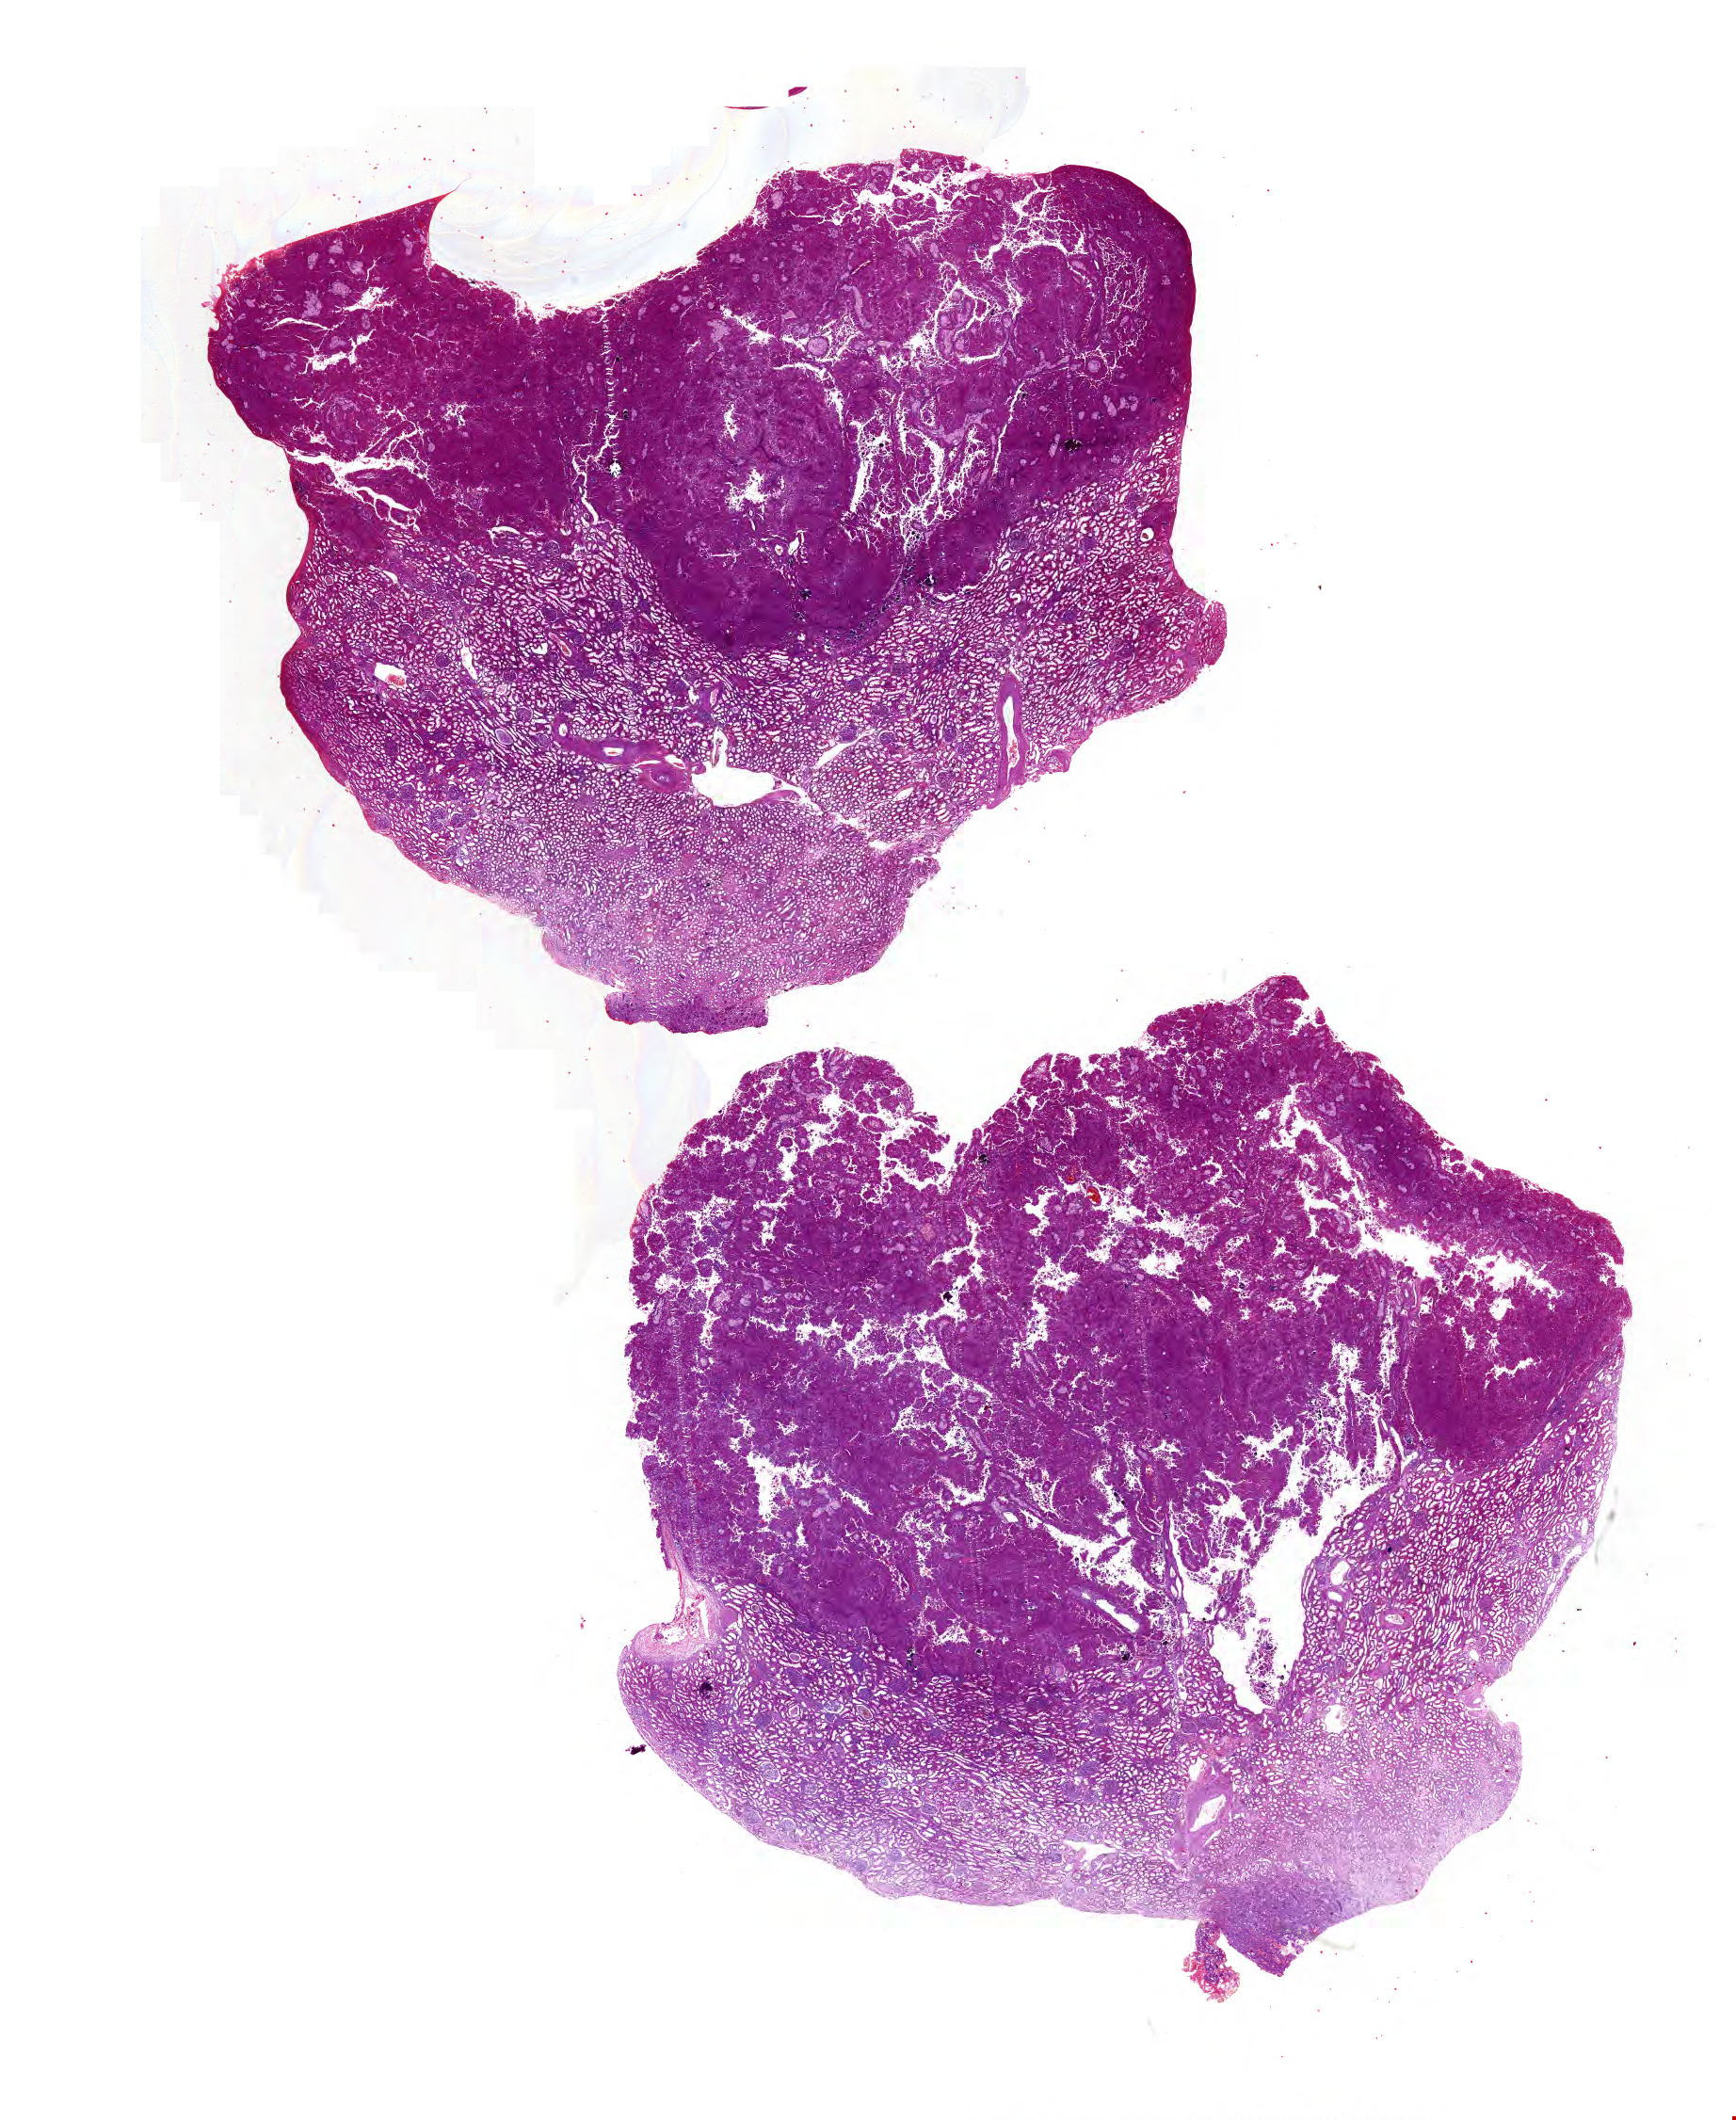
Whole-slide histology image, H&E-stained — shown as a low-resolution overview of the whole scanned area (about 23.0 x 28.0 mm); formalin-fixed paraffin-embedded (FFPE) diagnostic section; sample: primary tumour, kidney. Male patient; age at initial diagnosis 64 years.
Histologic diagnosis: Papillary adenocarcinoma, NOS.